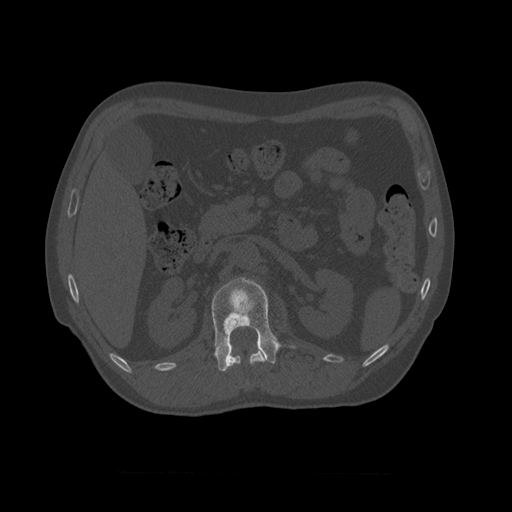
CT including the spine, one axial slice; position 360 of 450 along the scan axis; reconstruction kernel STANDARD; 120 kVp; bone window (W 1800 / L 400 HU); 1.25 mm slice thickness; 512 × 512 image matrix, field of view 405 × 405 mm. Patient age 75 years. Case-level facts recorded for this patient, not image findings: primary cancer: prostate.
Annotated regions visible in this slice (semi-automatically segmented with operator editing):
- L1 vertebra: bounding box (x1, y1, x2, y2) in pixels: (212, 277, 296, 372)
- T10 vertebra: (220, 340, 265, 371)
- T11 vertebra: (226, 351, 266, 384)